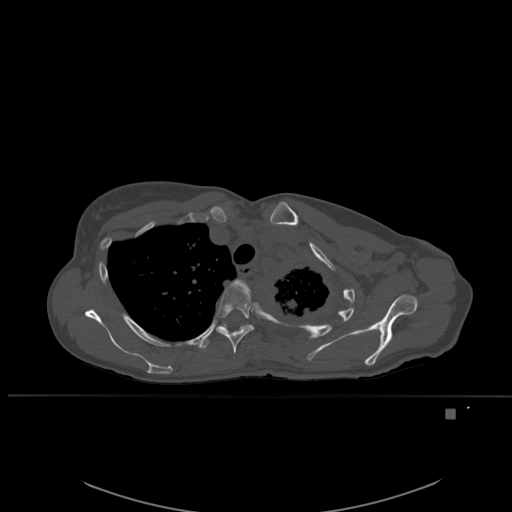
CT including the spine, one axial slice. Slice 411 of 537 in the series (ordered by position). Bone window (W 1800 / L 400 HU). 512 × 512 image matrix, field of view 440 × 440 mm. Female patient, age 45 years. From the clinical record (not read from this slice): primary cancer: lung.
Outlined on this slice (semi-automatically segmented with operator editing):
- T3 vertebra: box from (x=236, y=279) to (x=251, y=294) px
- T4 vertebra: (x=214, y=283)–(x=254, y=354)
- T5 vertebra: (x=197, y=324)–(x=250, y=349)